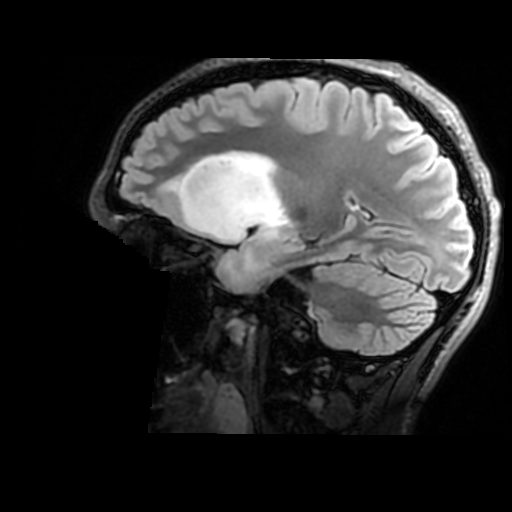
Brain MRI from a brain-tumour surgery series, one sagittal slice. Slice 109 of 176 in the series (ordered by position). T2 FLAIR. 1 mm slice thickness. 512 × 512 image matrix, field of view 240 × 240 mm. From the clinical record (not read from this slice): histopathology: Astrocytoma; WHO grade: 2; IDH mutation: yes; tumour location: Right Insular.
Structures marked on this image (outlined manually by an expert reader):
- tumour: bounding box [x1, y1, x2, y2] px = [174, 151, 289, 286]